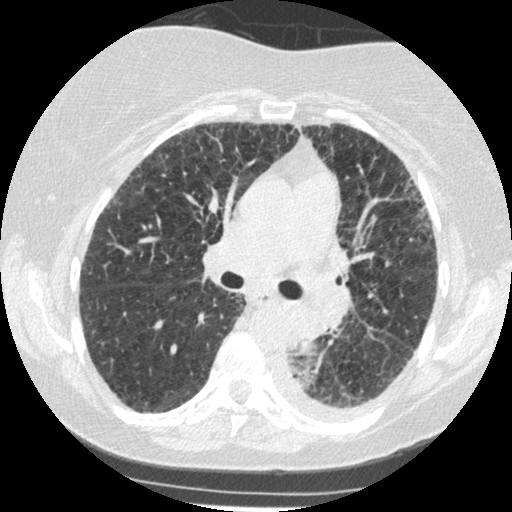
Low-dose screening chest CT, axial slice. Third annual screen. Lung window (W 1500 / L -600 HU). Standard (soft-tissue) reconstruction kernel (STANDARD). Slice 184 of 341 in the series. Female, age 60 years at enrolment.
• Expert reader's lesion annotation, bounding box <269,308,342,373> (left, top, right, bottom; pixels).
• The exam's reader record, not a measurement of the box and not confirmed to be the same lesion: non-calcified nodule or mass ≥4 mm, left lower lobe, 54 × 38 mm, smooth margins, soft tissue attenuation, pre-existing on the prior screen: yes; interval growth: yes.
• Lung cancer was diagnosed 15 days after this screen: small cell carcinoma, NOS, left lower lobe, undifferentiated (G4), stage IV (AJCC 6th edition), 69 mm at pathology.